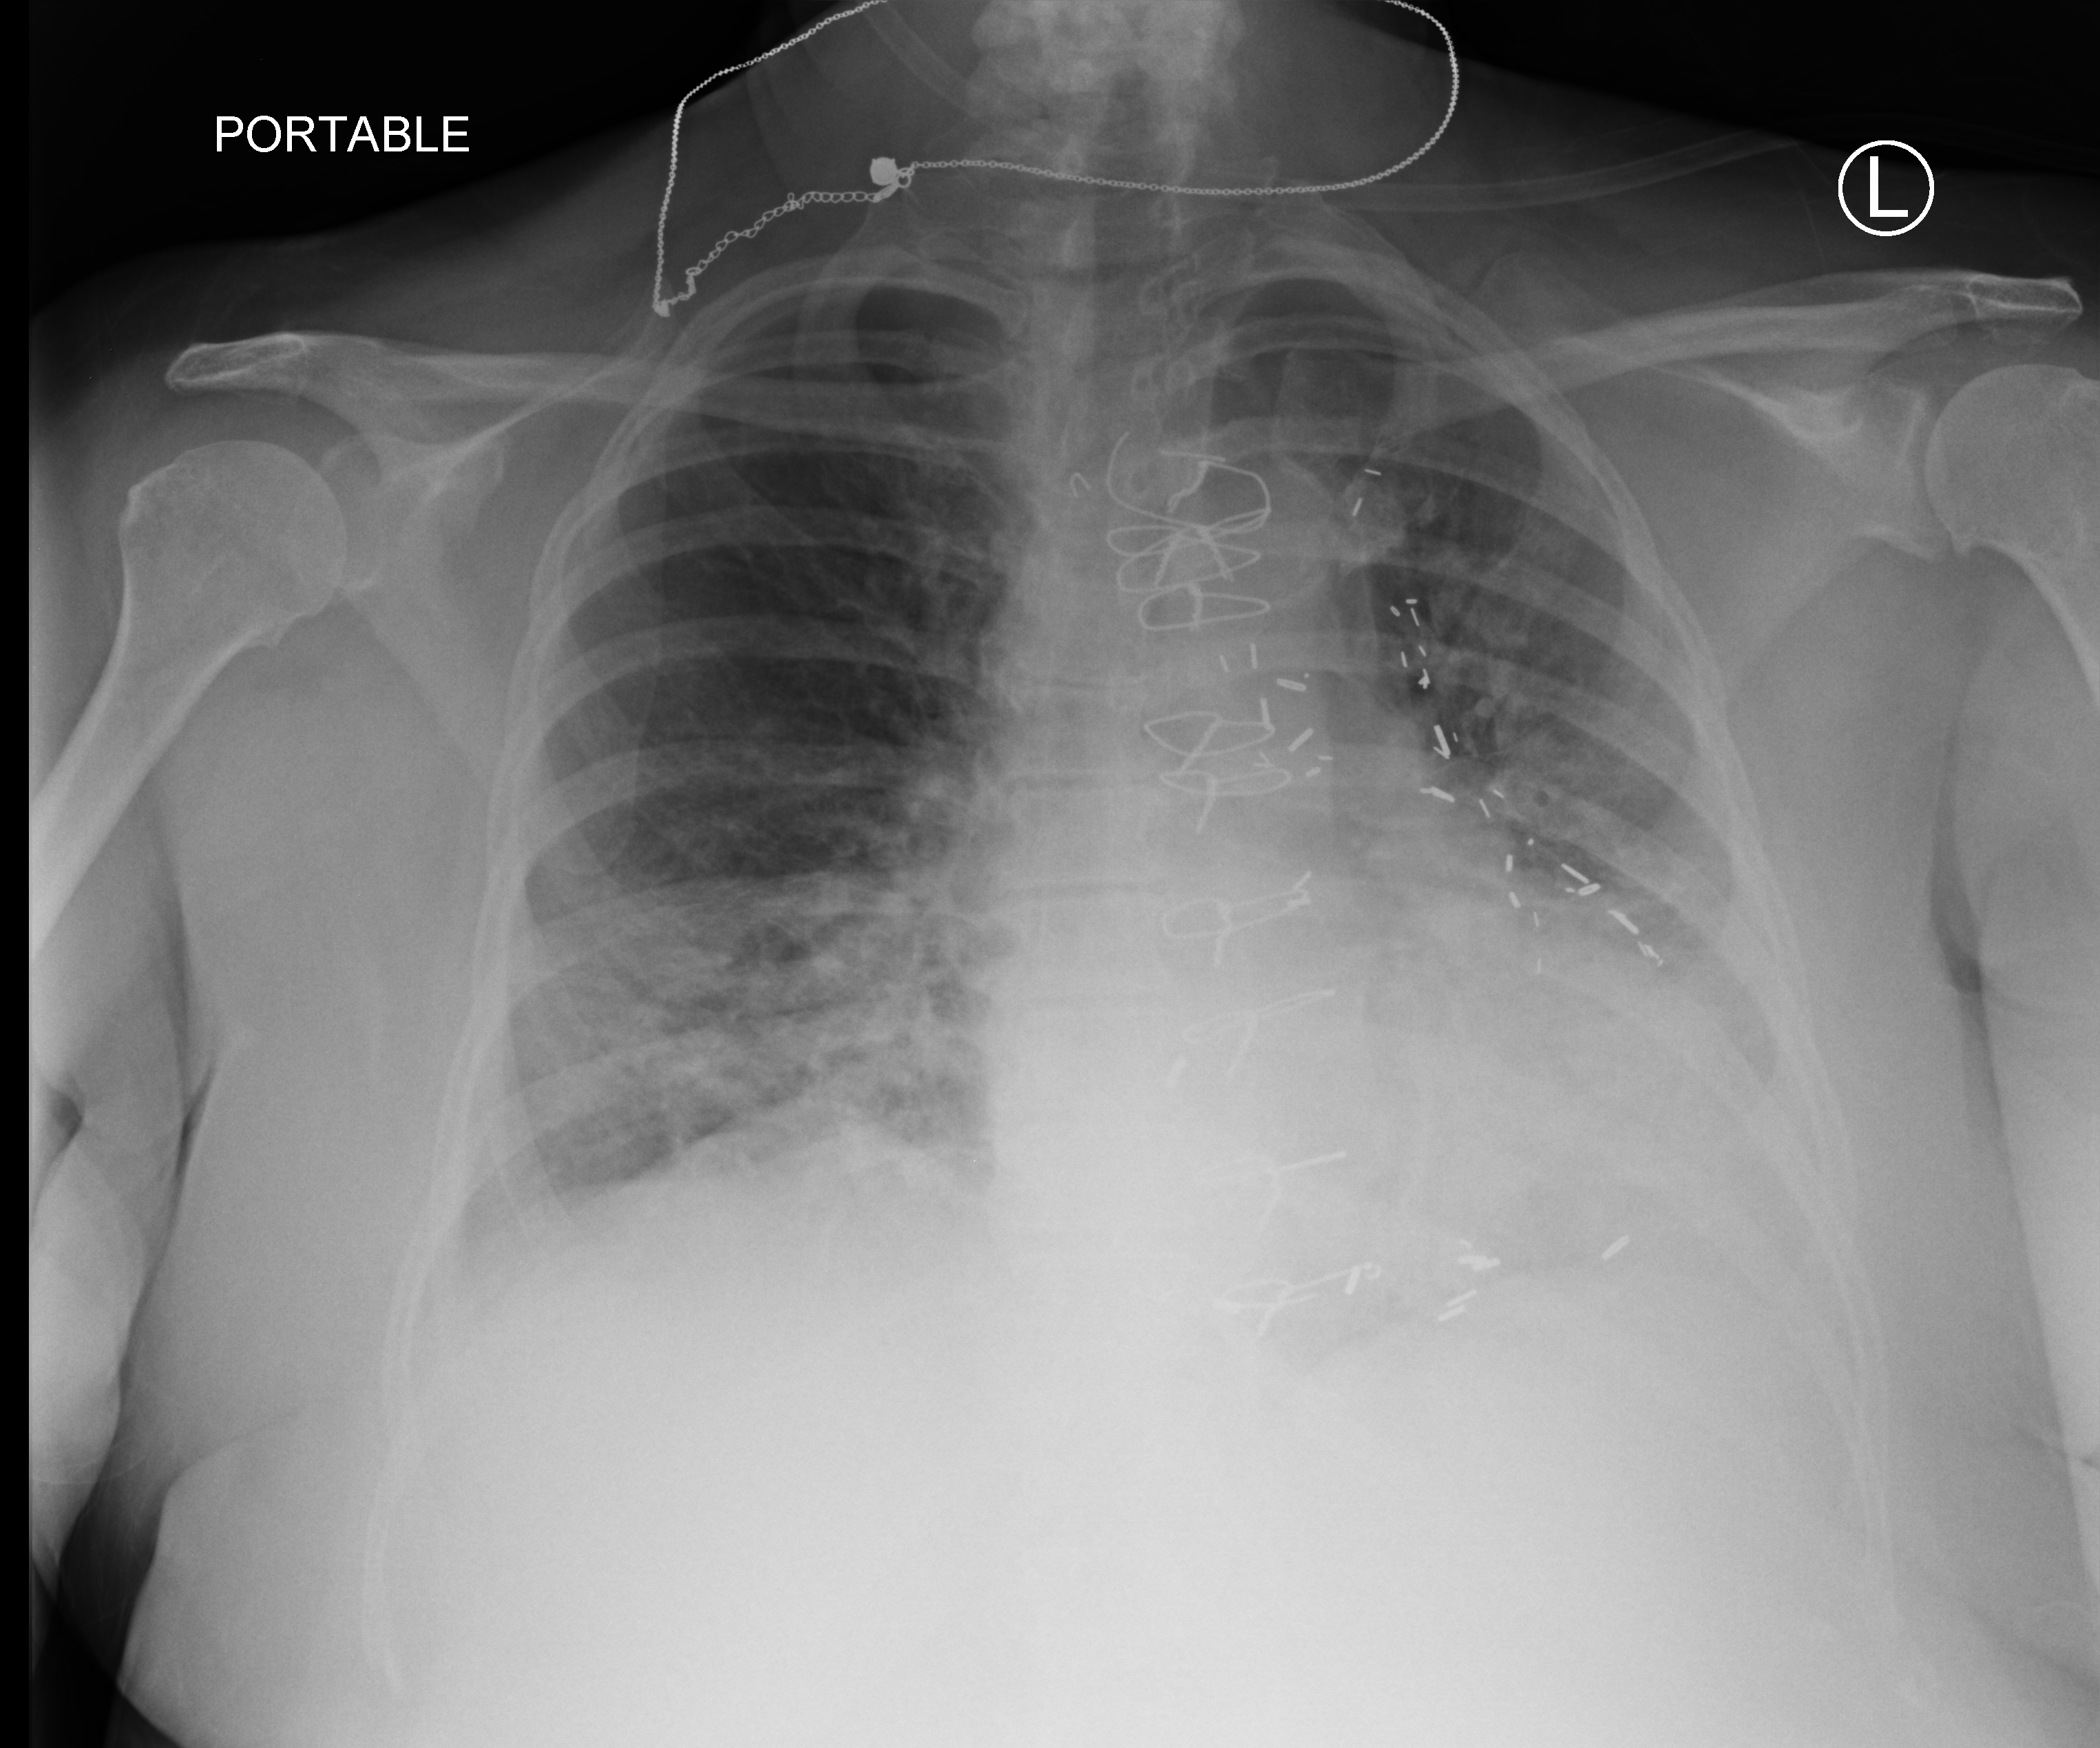
Bedside chest radiograph (computed radiography); anteroposterior (AP) projection. Patient hospitalised with COVID-19; female, aged 60–74 years.
Admission-level facts for this patient (not findings on this image; timing relative to this image not recorded): mechanically ventilated during this hospital stay: yes; COPD (admission record): no; hypertension (admission record): yes.